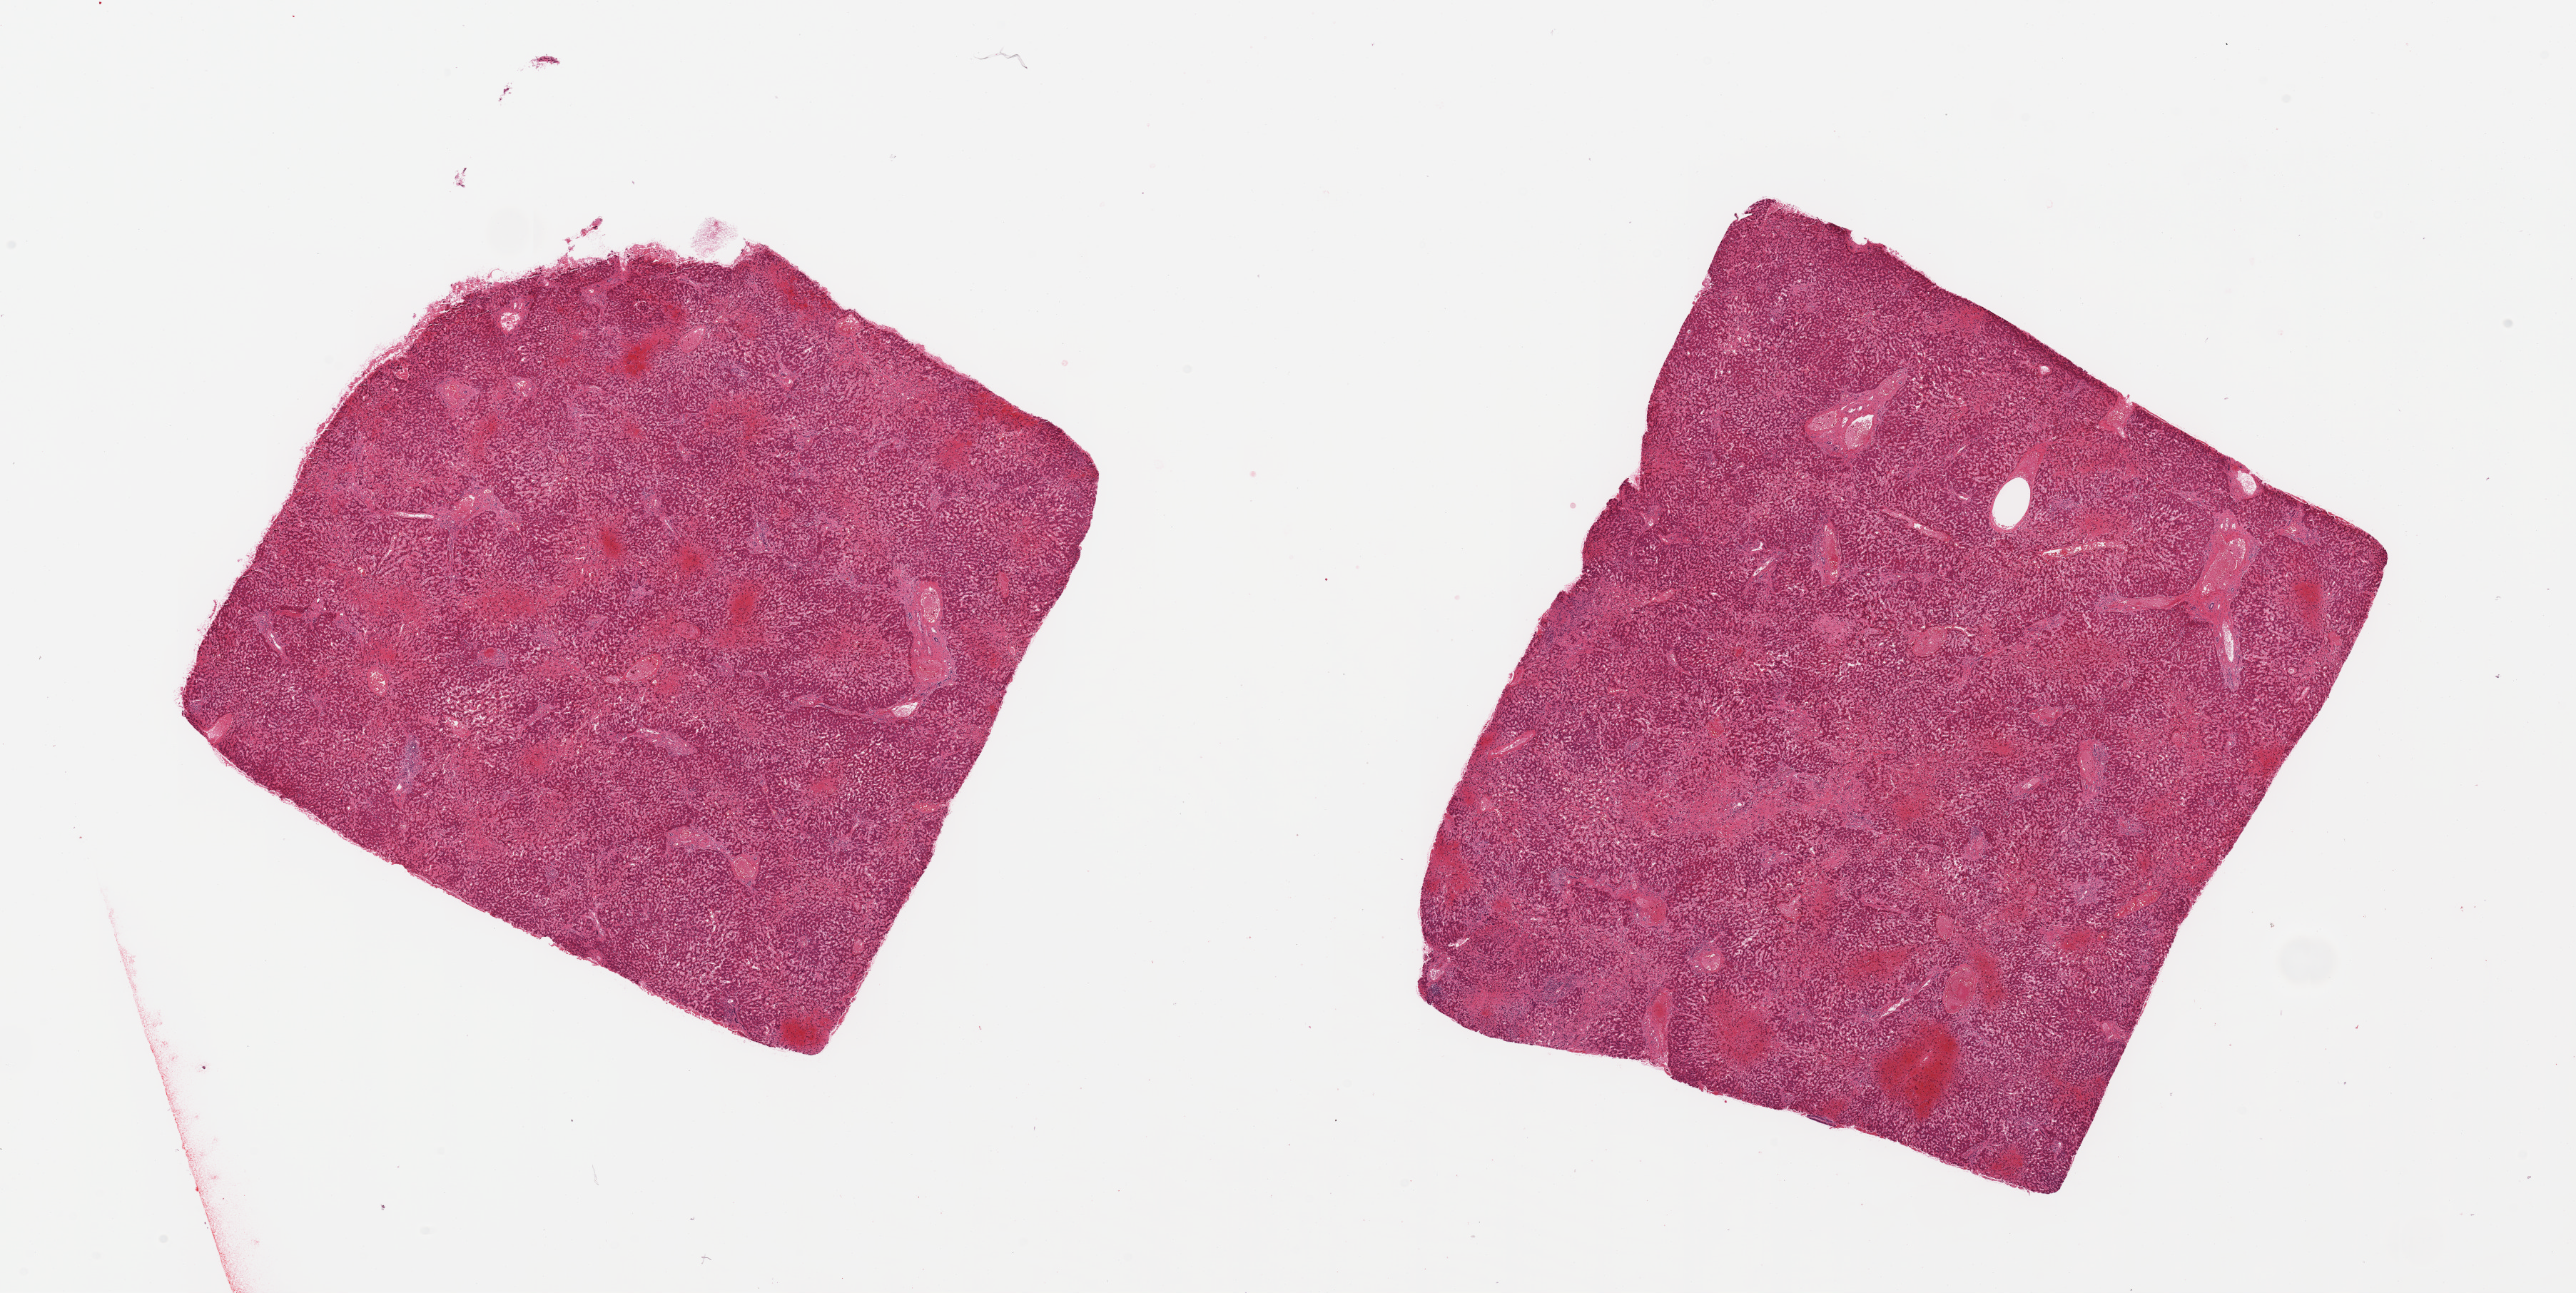
Digitized haematoxylin and eosin-stained section, brightfield — whole scanned area (about 28.5 x 14.3 mm) shown as a low-resolution overview, PAXgene-fixed paraffin-embedded (PFPE) section, sampled site (target tissue): liver, tissue donor sample. Donor: male.
- pathologist's review note for this sample: 2 pieces; extensive centrilobular sinusoidal congestion with cord cell loss